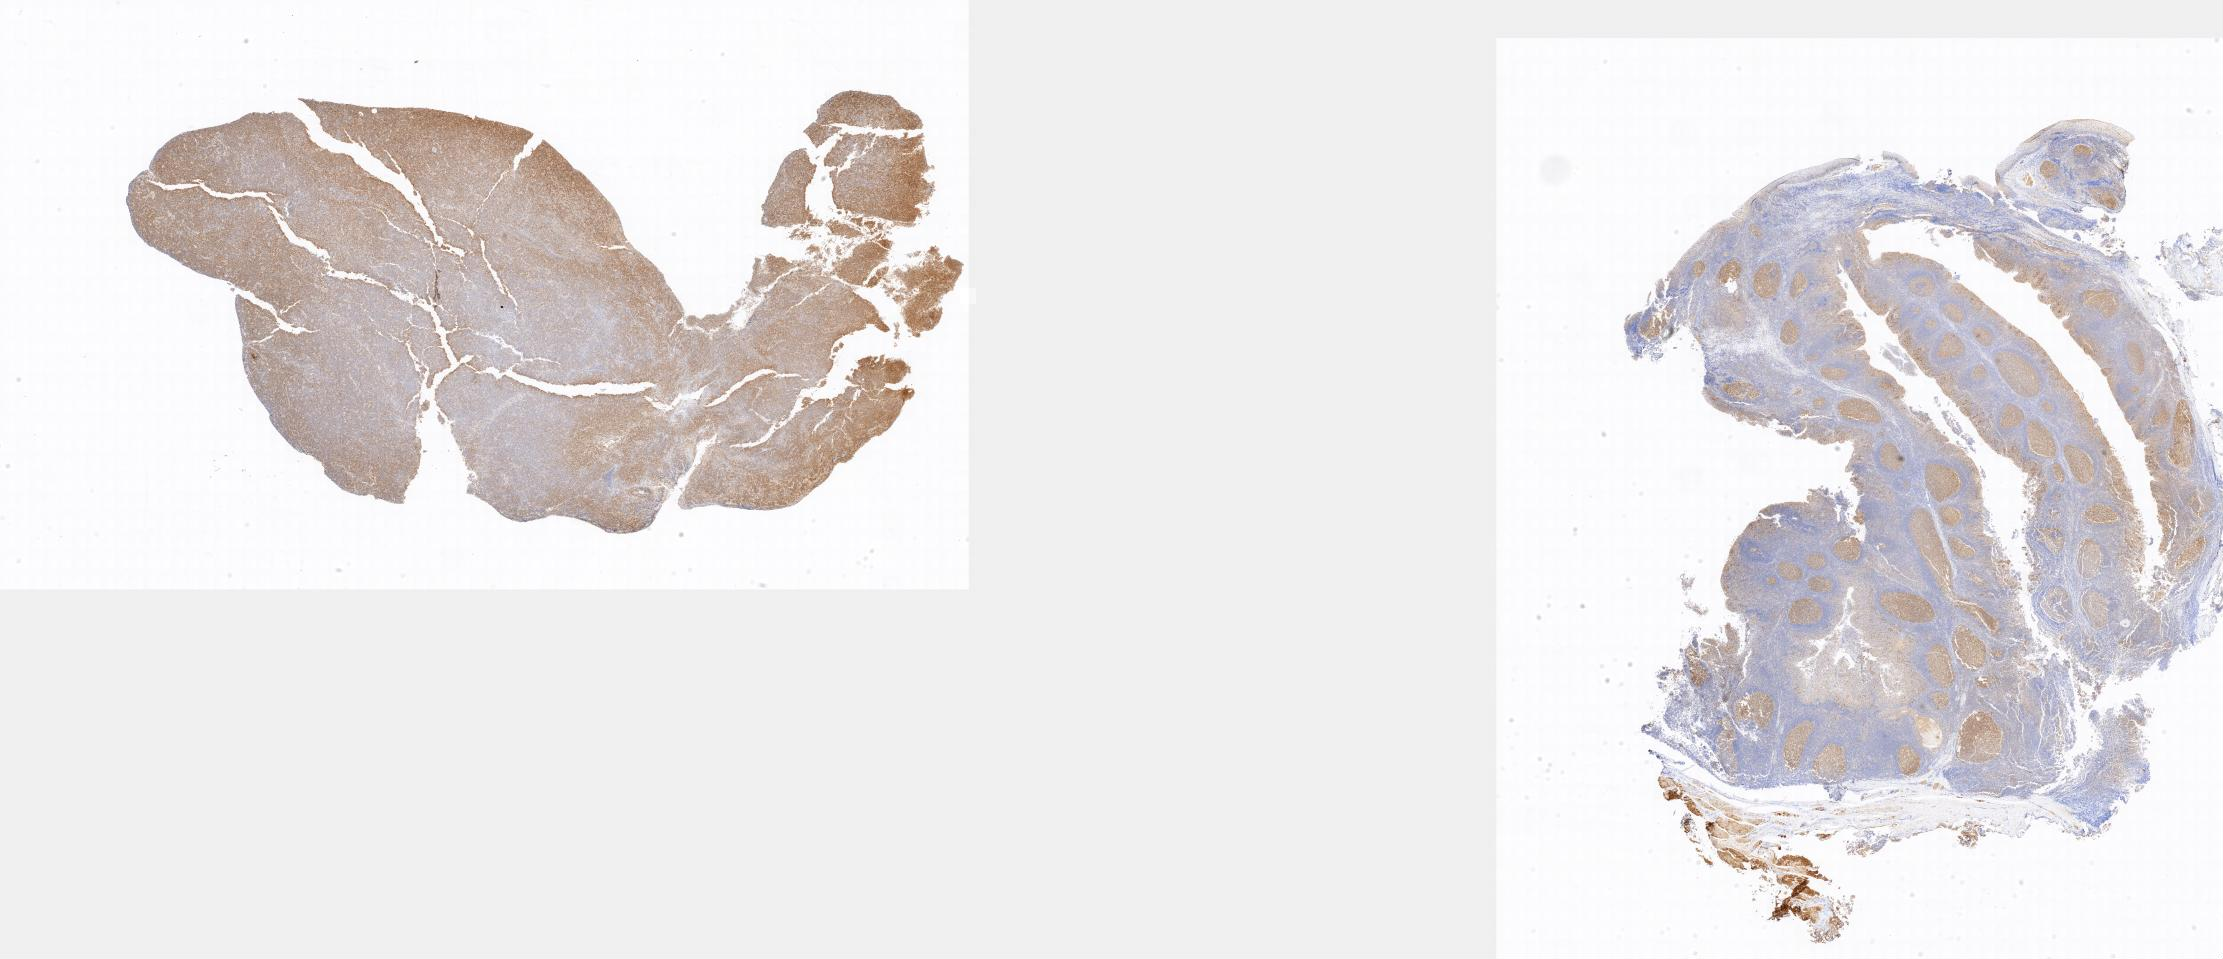
Immunohistochemistry (IHC) whole-slide image stained for BCL6 — whole scanned area shown as a low-resolution overview, tumor tissue, anatomic site: lymph node of head and neck. Male patient; age at initial diagnosis 5 years.
Diagnosis: Burkitt lymphoma, NOS.